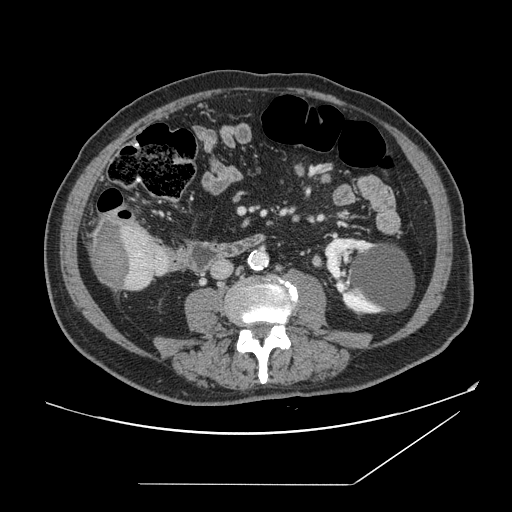
Contrast-enhanced abdominal CT, one axial slice; slice 33 of 166 in the series (ordered by position); intravenous contrast given; soft-tissue window (W 400 / L 40 HU); 2.5 mm slice thickness; 512 × 512 image matrix, field of view 416 × 416 mm. Male patient, age 80 years. Case-level facts recorded for this patient, not image findings: diagnosis: colorectal cancer liver metastases, imaged before liver resection; multiple liver metastases: no.
Outlined on this slice (manually delineated by an expert):
- liver: bounding box (x1, y1, x2, y2) in pixels: (89, 219, 168, 291)
- liver metastasis: (92, 222, 132, 288)